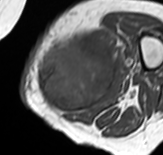
MRI of an extremity soft-tissue mass, one axial slice. Position 24 of 65 along the scan axis. MR volume resampled by the dataset authors to the PET/CT grid (not the native acquisition matrix). 3.27 mm slice thickness. 163 × 155 image matrix. Female patient. Case-level facts recorded for this patient, not image findings: histological type: pleomorphic leiomyosarcoma; grade: high; site of the primary tumour: left thigh.
Annotated regions visible in this slice (expert contour drawn on MRI and transferred to this co-registered scan by the dataset authors):
- gross tumour volume including surrounding oedema: bounding box (x1, y1, x2, y2) in pixels: (35, 31, 122, 112)
- gross tumour volume (mass): (35, 40, 116, 112)